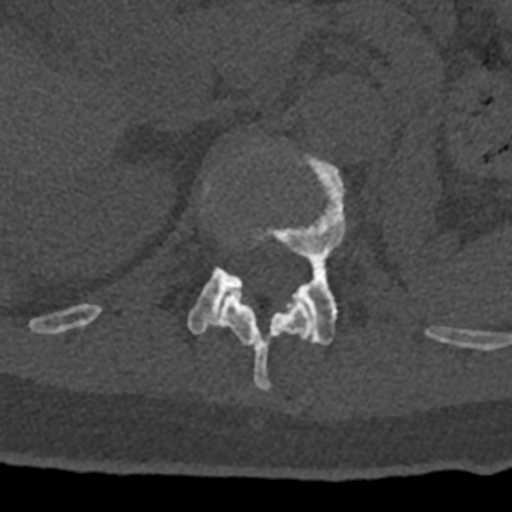
CT including the spine, one axial slice; position 462 of 797 along the scan axis; reconstruction kernel Br40s/3; bone window (W 1800 / L 400 HU); 0.5 mm slice thickness; 512 × 512 image matrix, field of view 160 × 160 mm. Male patient, age 74 years. From the clinical record (not read from this slice): primary cancer: renal; vertebrae with lytic lesions (as recorded): T10, L1, L2, L3, L4, L5.
Annotated regions visible in this slice (semi-automatically segmented with operator editing):
- L1 vertebra: box from (x=187, y=154) to (x=346, y=346) px
- T12 vertebra: (x=70, y=183)–(x=432, y=391)